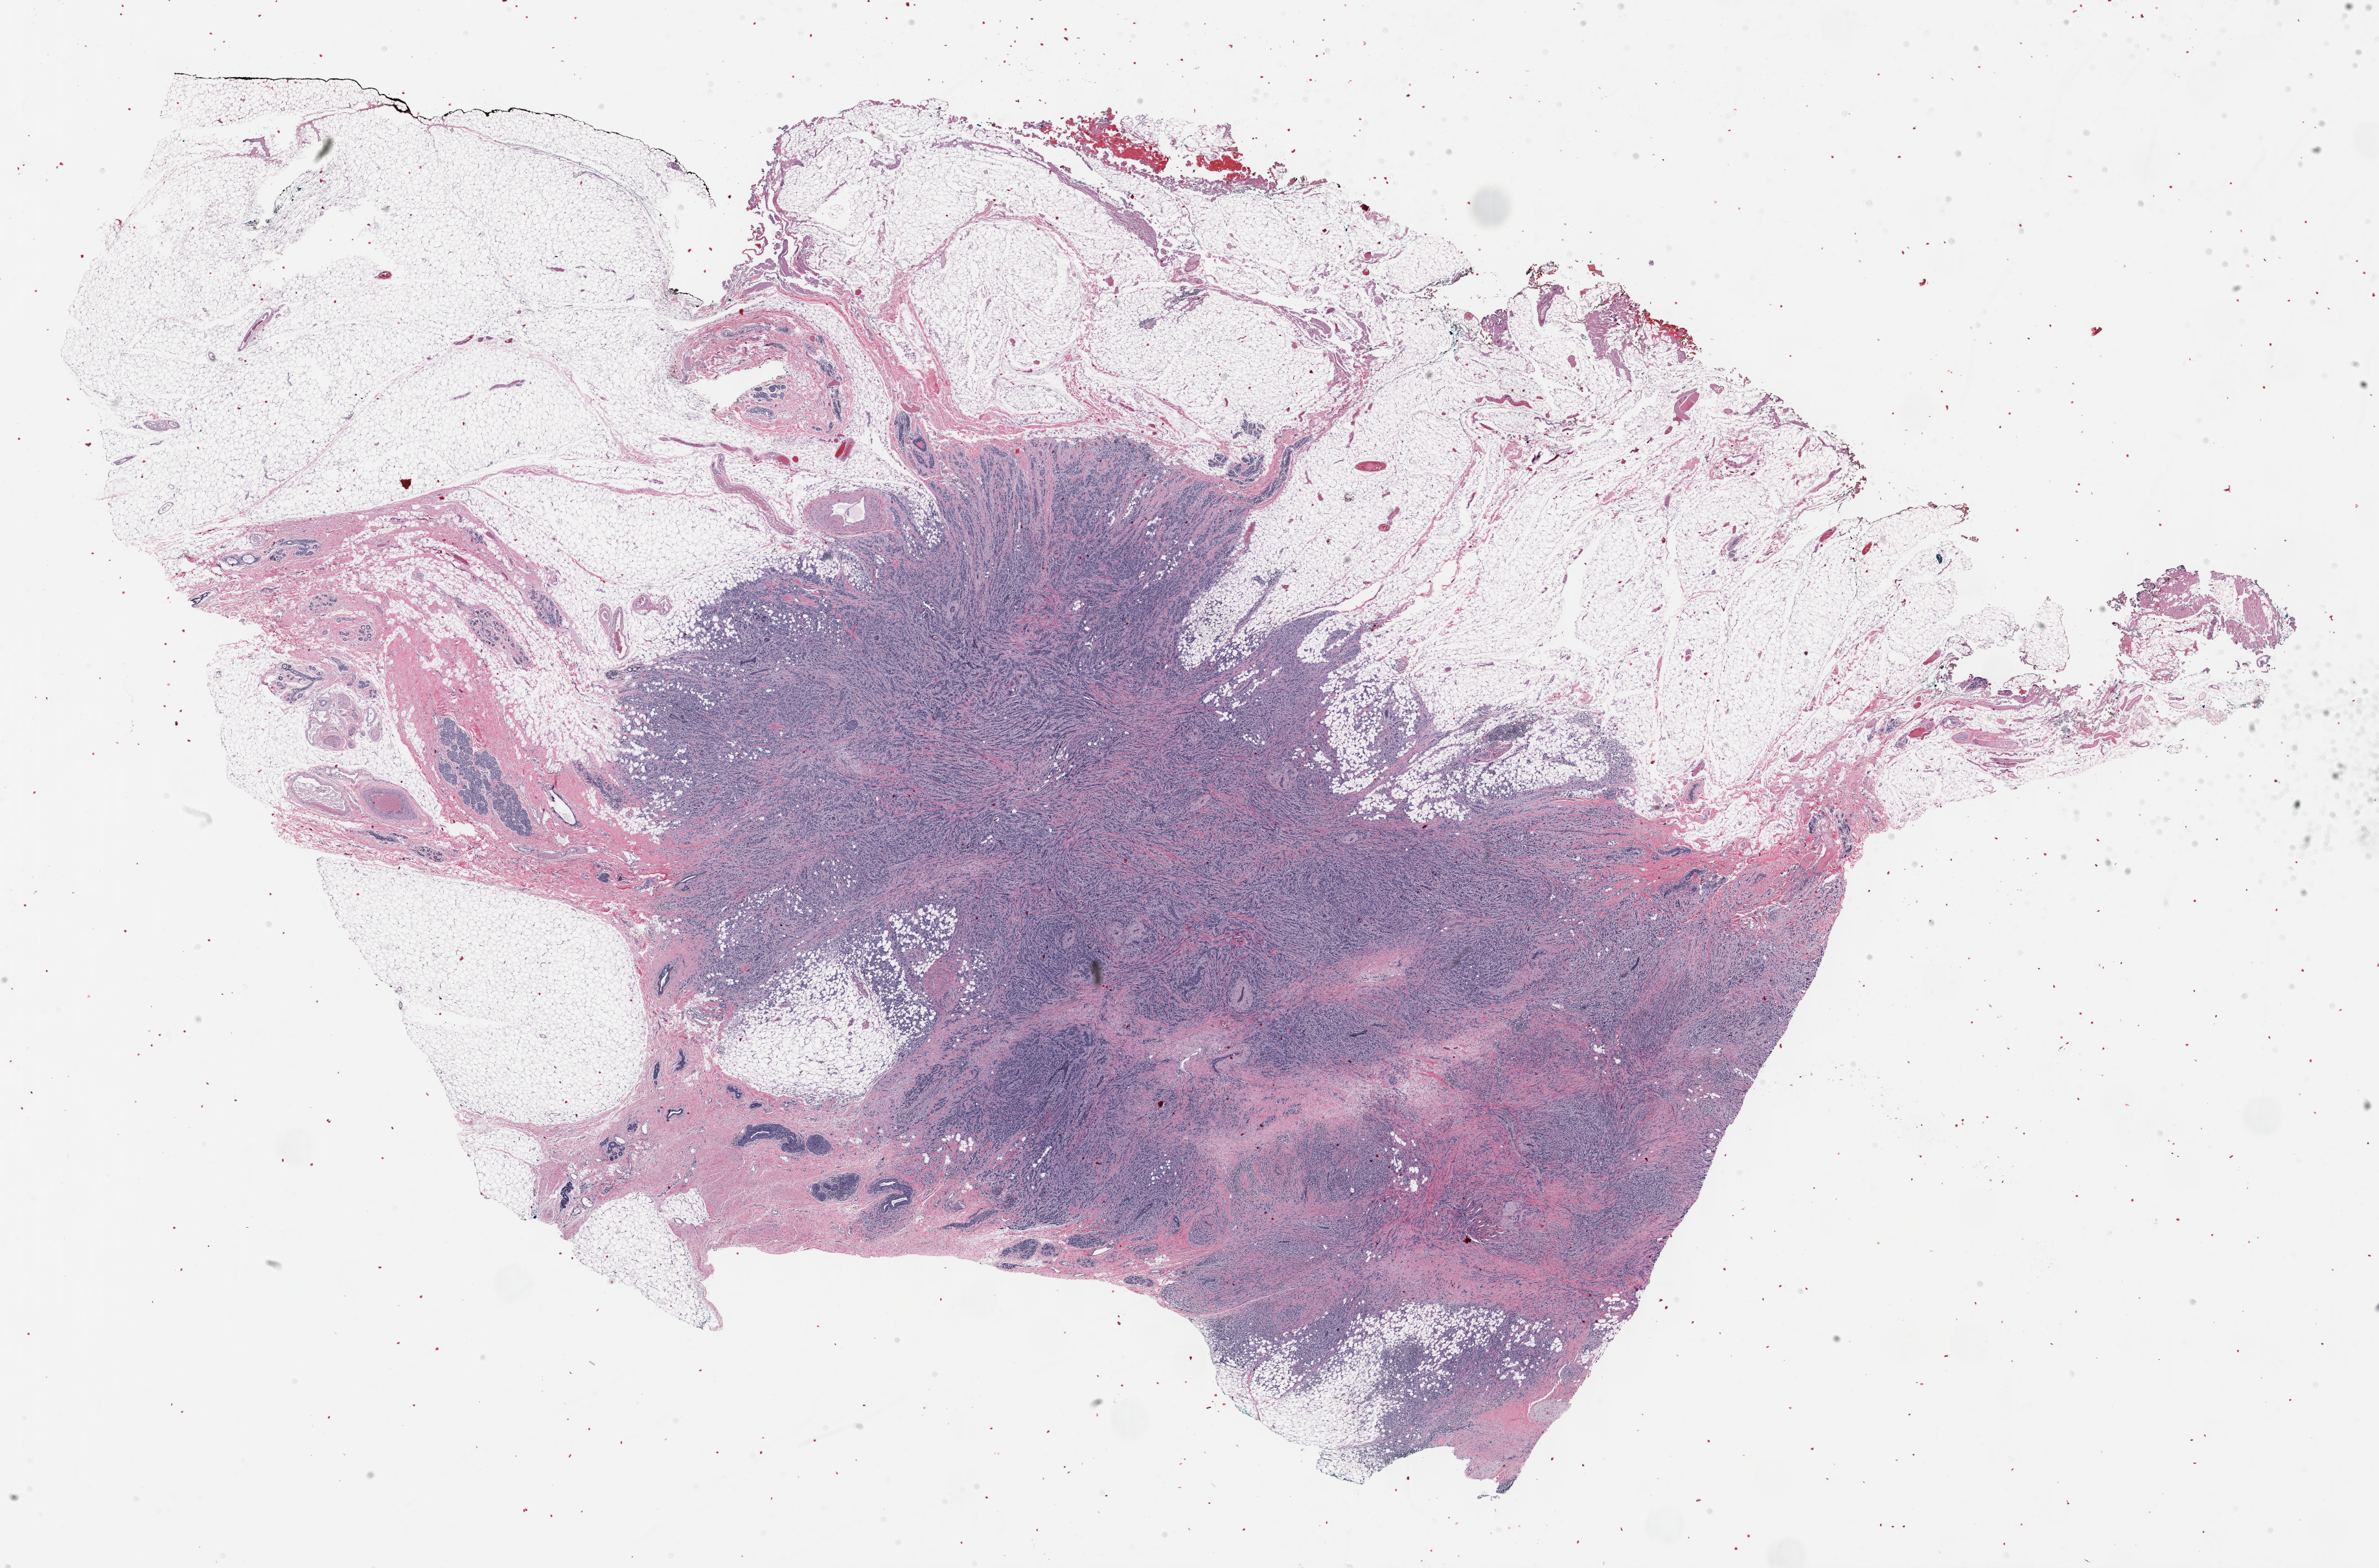
Whole-slide histology image, H&E-stained, whole scanned area (about 29.7 x 19.6 mm, acquisition: 40x scan) shown as a low-resolution overview, formalin-fixed paraffin-embedded (FFPE) diagnostic section, sample: primary tumour, breast. Female patient; age at initial diagnosis 44 years.
AJCC pathologic stage: IIB (7th edition). Laterality: right. TNM: T2 N1mi MX. Diagnosis: Lobular carcinoma, NOS.